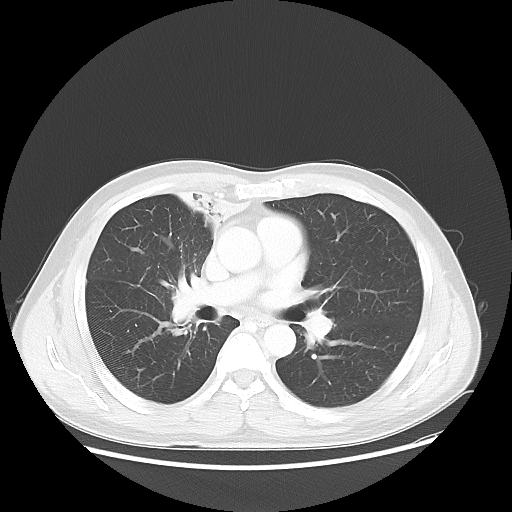
Chest CT, one axial slice; position 30 of 56 along the scan axis; reconstruction kernel LUNG; lung window (W 1500 / L -600 HU); 5 mm slice thickness; 512 × 512 image matrix, field of view 398 × 398 mm. Male patient, age 60 years. From the clinical record (not read from this slice): clinical TNM (as recorded): T2a N1 M0.
Annotated regions visible in this slice (rectangle marked by the reading radiologist):
- lung tumour (recorded histology: squamous cell carcinoma): bounding box [x1, y1, x2, y2] px = [177, 186, 254, 242]